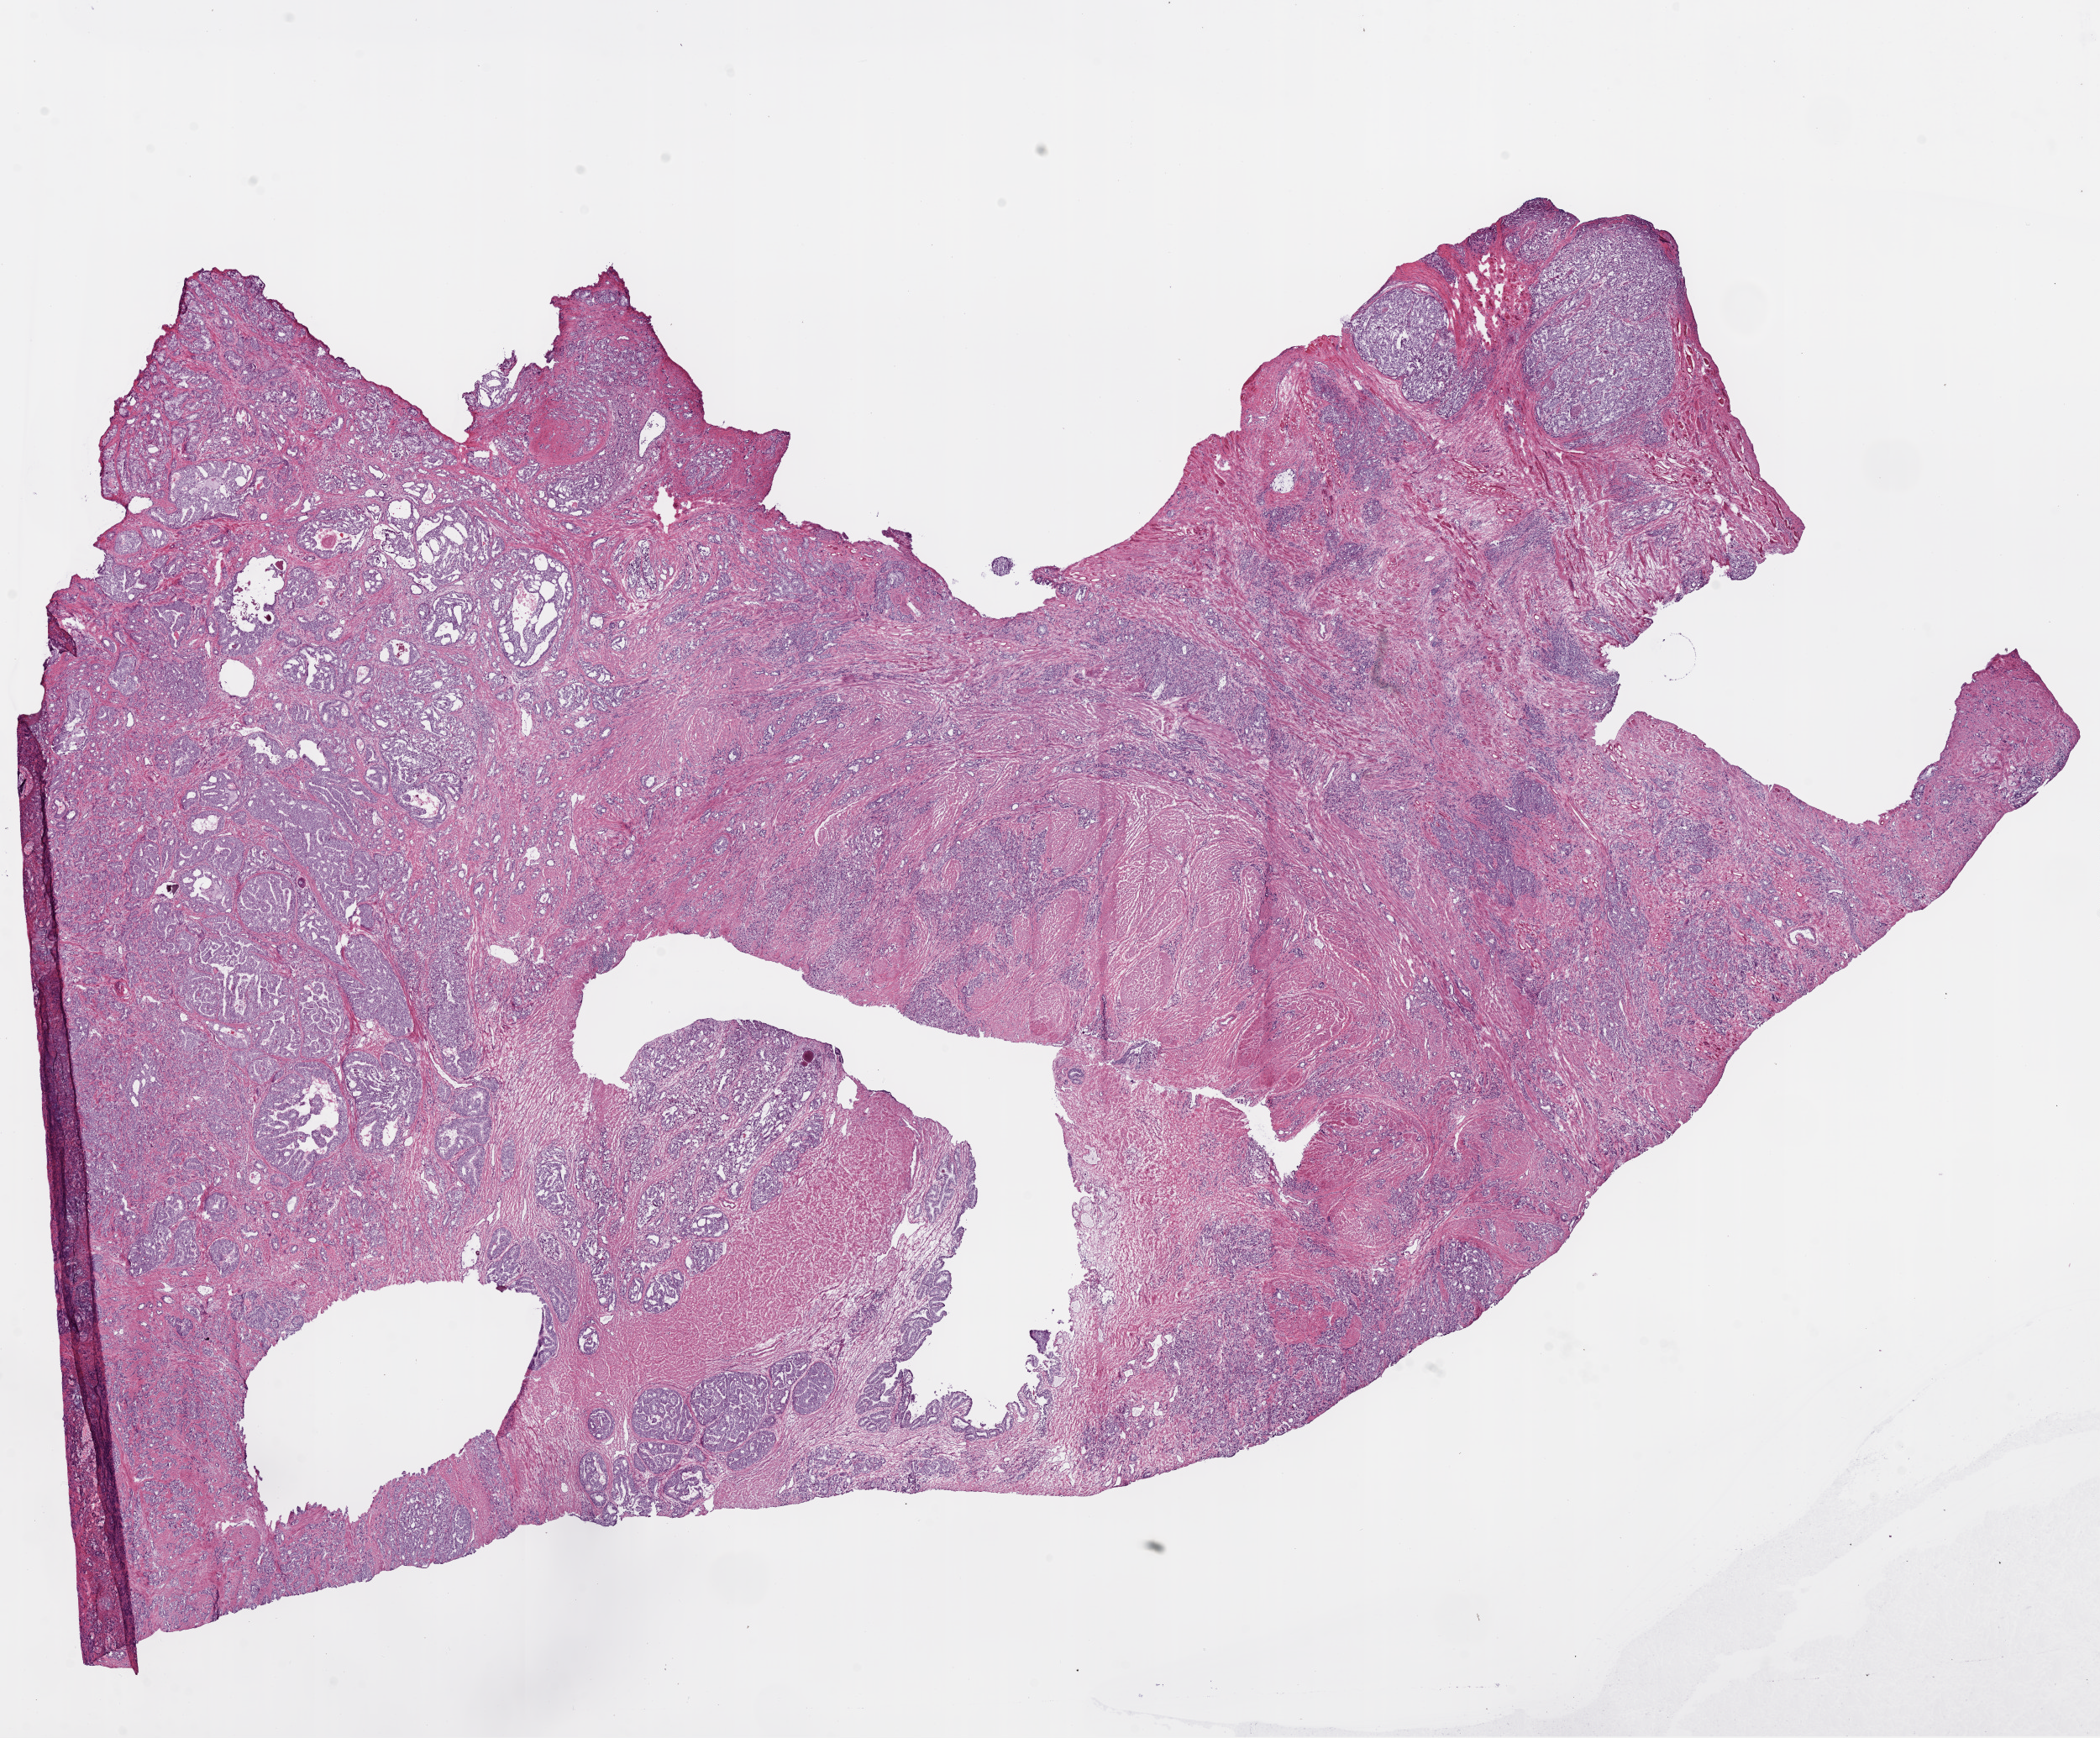
Whole-slide histology image, H&E-stained — a low-resolution overview of the entire scanned area, about 20.1 x 16.6 mm (slide scanned at 20x). Frozen section from the bottom of the tissue portion. Sample: primary tumour, prostate. Patient: male, age at initial diagnosis 66 years. Gleason score: 9 (4+5). Composition of this section per pathologist review: tumour cells 55%, tumour nuclei 60%, normal cells 15%, stromal cells 29%, necrosis 1%. Inflammatory infiltration, as recorded: lymphocyte infiltration 2%, monocyte infiltration 0%, neutrophil infiltration 0%.
• lymph nodes positive (case pathology): 0 of 3 examined
• histologic diagnosis: Acinar cell carcinoma (prostate gland)